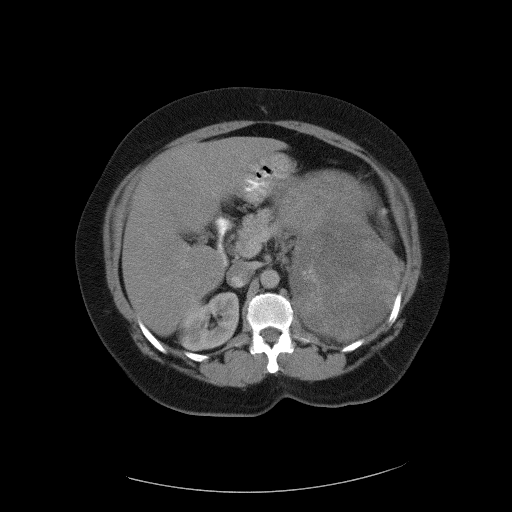
Contrast-enhanced abdominal CT, one axial slice; position 66 of 90 along the scan axis; 120 kVp; intravenous contrast given; soft-tissue window (W 400 / L 40 HU); 512 × 512 image matrix, field of view 480 × 480 mm. Patient: female, 55 years. Case-level facts recorded for this patient, not image findings: diagnosis: adrenocortical carcinoma; tumour side: left adrenal.
Structures marked on this image (semi-automatic segmentation, software-assisted and operator-edited):
- mass: bounding box (x1, y1, x2, y2) in pixels: (280, 169, 399, 338)